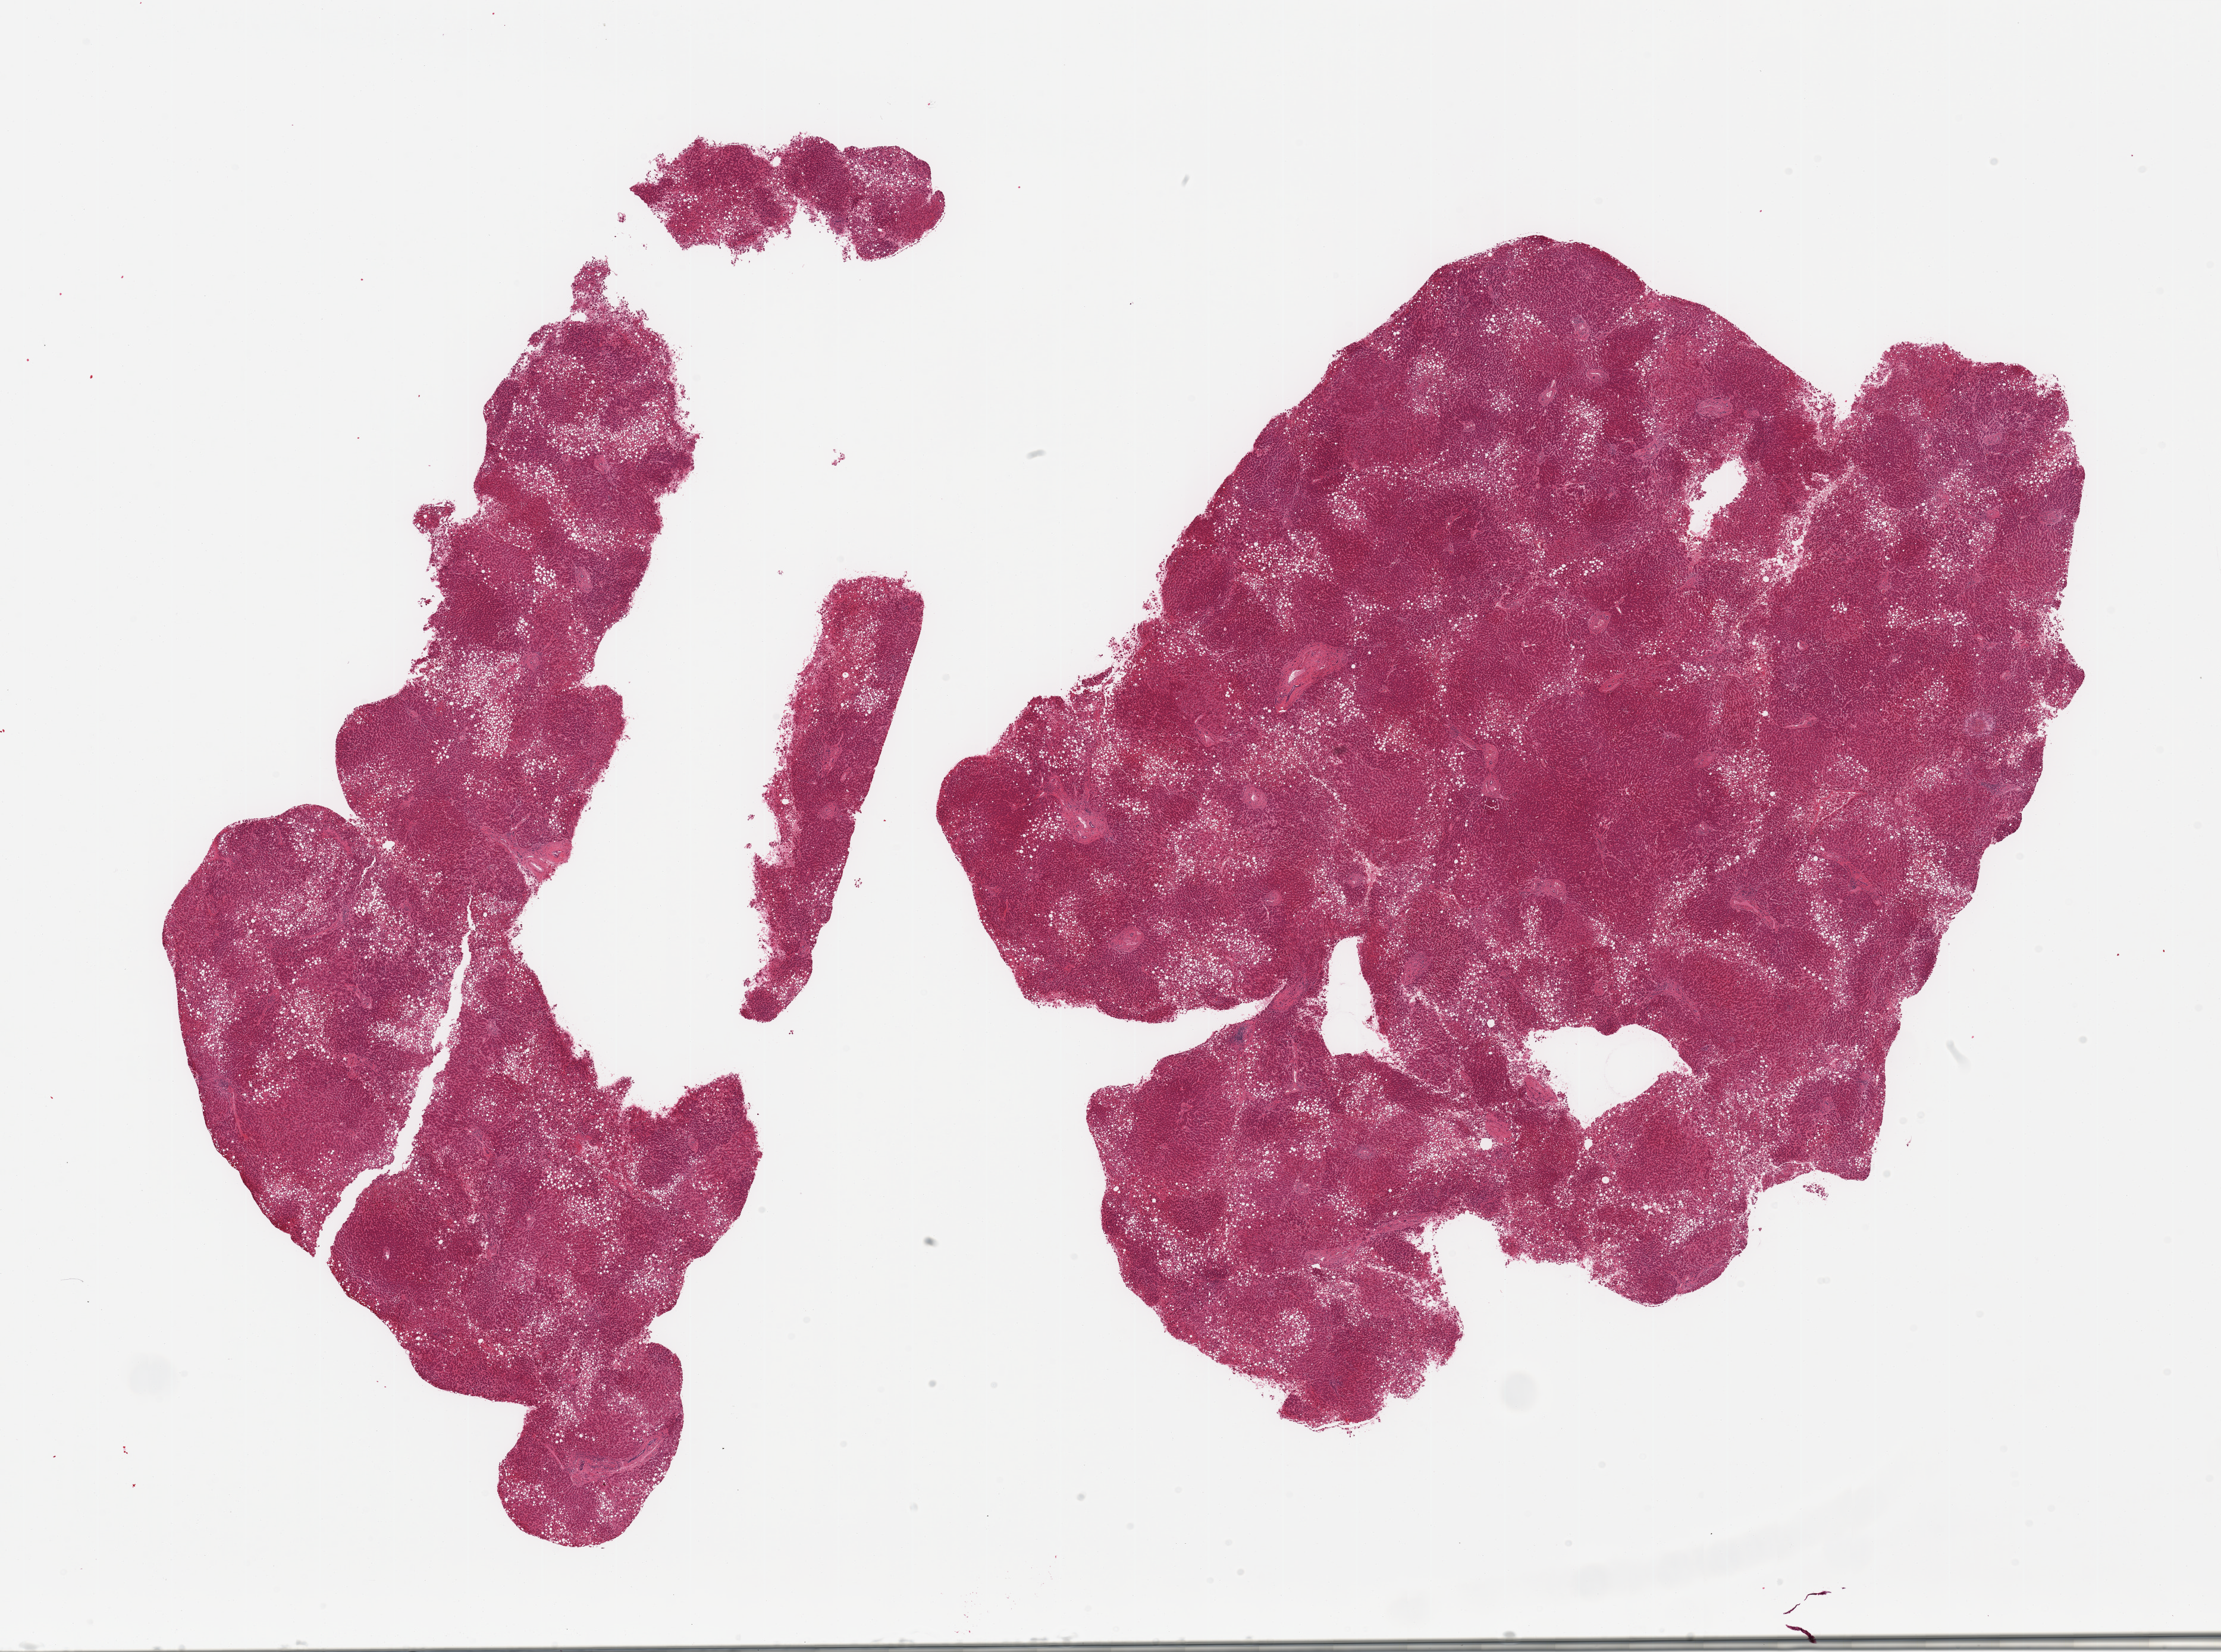
Digitized haematoxylin and eosin-stained section, a low-resolution overview of the entire scanned area, about 29.5 x 22.0 mm; PAXgene-fixed paraffin-embedded (PFPE) section; section of liver (target tissue); donor tissue sample. Male donor.
Review note (as recorded): 2 pieces, macrovesicular steatosis invoves ~40% of parenchyma; moderate passive congestion.